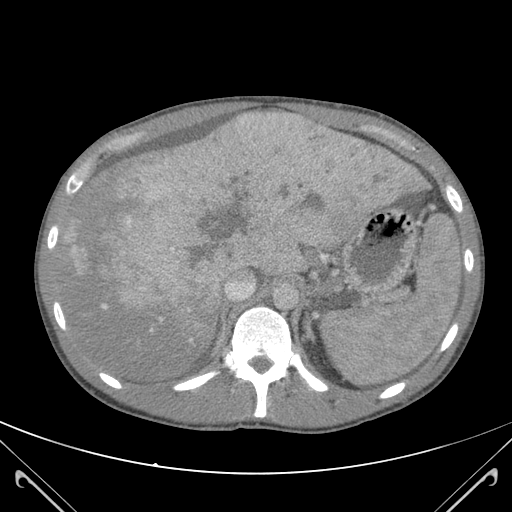
Contrast-enhanced abdominal CT (liver protocol), one axial slice. Slice 84 of 118 in the series (ordered by position). Soft-tissue window (W 400 / L 40 HU). 512 × 512 image matrix, field of view 380 × 380 mm. From the clinical record (not read from this slice): diagnosis: hepatocellular carcinoma (patient treated with transarterial chemoembolisation; whether this scan precedes or follows treatment is not stated here); TNM stage (as recorded): Stage-IIIB; Child-Pugh class: A.
Annotated regions visible in this slice (semi-automatically segmented with operator editing):
- abdominal aorta: box from (x=273, y=284) to (x=298, y=308) px
- liver parenchyma outside the tumour (the mass and vessels are separate outlines, so this box may not span the whole liver): (x=60, y=116)–(x=423, y=378)
- mass: (x=94, y=120)–(x=413, y=330)
- liver vessels: (x=65, y=116)–(x=394, y=341)